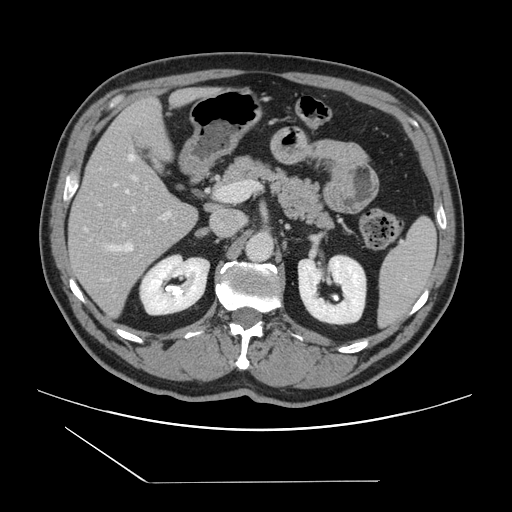
Contrast-enhanced abdominal CT, one axial slice. Slice 76 of 157 in the series (ordered by position). 120 kVp. Intravenous contrast given. Soft-tissue window (W 400 / L 40 HU). 2.5 mm slice thickness. 512 × 512 image matrix, field of view 407 × 407 mm. Male patient, age 61 years. Case-level facts recorded for this patient, not image findings: diagnosis: colorectal cancer liver metastases, imaged before liver resection; multiple liver metastases: yes; largest metastasis: 5.5 cm; chemotherapy before resection: no.
Annotated regions visible in this slice (manually delineated by an expert):
- hepatic veins: bounding box <85,154,135,251> (left, top, right, bottom; pixels)
- liver: <69,90,206,320>
- planned liver remnant (the part of the liver to remain after resection): <71,90,204,220>
- portal vein (with intrahepatic branches): <100,176,171,225>